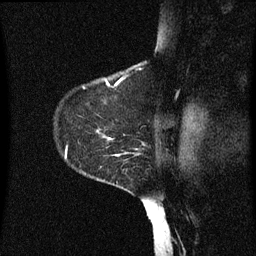
Breast MRI (dynamic contrast-enhanced), one sagittal slice; slice 48 of 60 in the series (ordered by position); dynamic contrast-enhanced series, image 2 of 3 at this slice position (ordered by acquisition); 1.5 T; TE 4.2 ms, TR 8 ms; 256 × 256 image matrix. Patient: female, 55 years.
Annotated regions visible in this slice (semi-automatically segmented with operator editing):
- analysis volume of interest (the breast-tissue region the enhancement analysis was run in; not a lesion): box from (x=54, y=124) to (x=149, y=183) px
- tumour enhancement mask (voxels above the 70 % enhancement threshold inside the analysis volume of interest): (x=102, y=134)–(x=125, y=167)